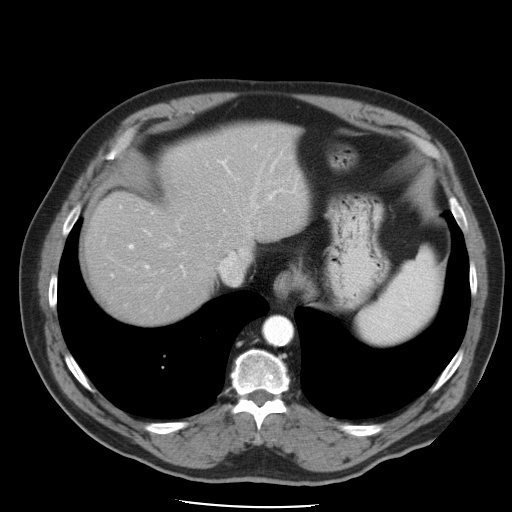
Contrast-enhanced abdominal CT, one axial slice; position 40 of 49 along the scan axis; reconstruction kernel STANDARD; 120 kVp; intravenous contrast given; soft-tissue window (W 400 / L 40 HU); 5 mm slice thickness; 512 × 512 image matrix, field of view 395 × 395 mm. Male patient, age 68 years. From the clinical record (not read from this slice): diagnosis: colorectal cancer liver metastases, imaged before liver resection; multiple liver metastases: yes; largest metastasis: 1.7 cm; chemotherapy before resection: yes.
Structures marked on this image (outlined manually by an expert reader):
- hepatic veins: bounding box <159,166,263,294> (left, top, right, bottom; pixels)
- liver: <87,124,309,323>
- planned liver remnant (the part of the liver to remain after resection): <87,124,309,324>
- portal vein (with intrahepatic branches): <112,145,298,277>